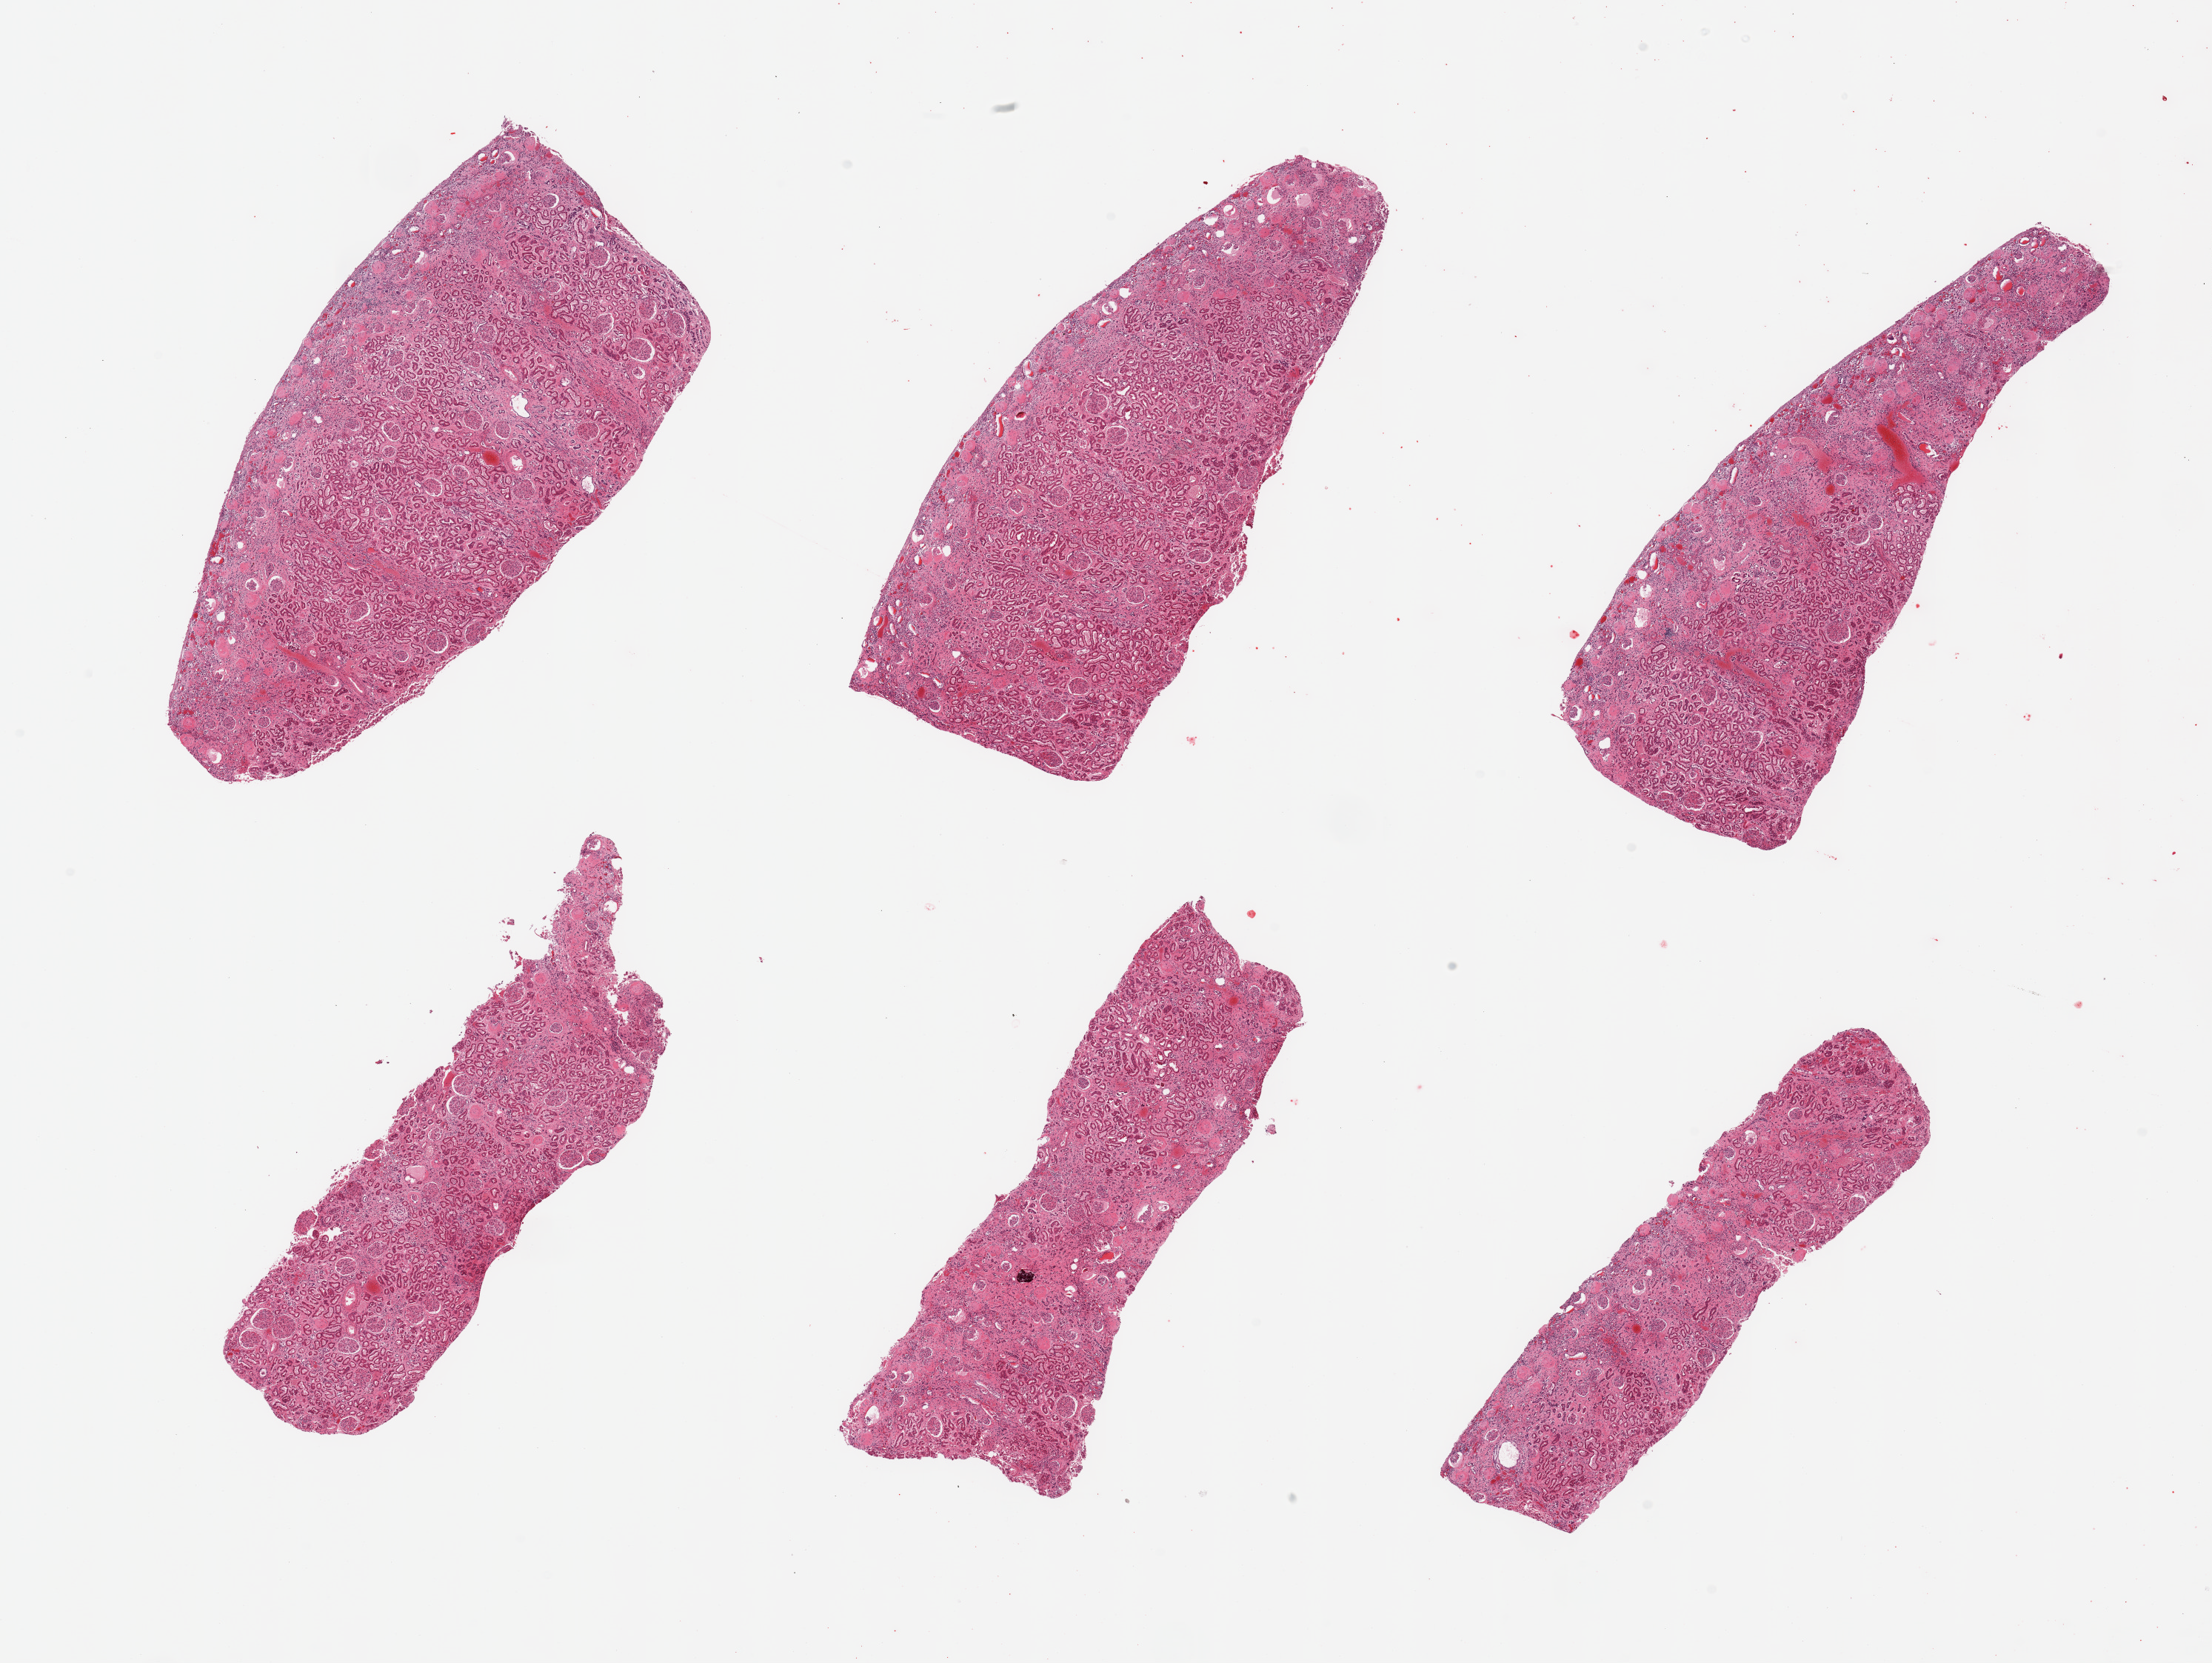
Digitized hematoxylin and eosin (H&E)-stained section — shown as a low-resolution overview of the whole scanned area (about 23.6 x 17.8 mm, acquisition: 20x scan); PAXgene-fixed, paraffin-embedded tissue; target tissue: renal cortex; tissue donor sample. Donor sex: female.
Review note (as recorded): 6 pieces; moderate to severe interstitial and glomerular fibrosis.